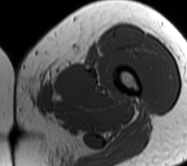
MRI of an extremity soft-tissue mass, one axial slice. Position 7 of 62 along the scan axis. MR volume resampled by the dataset authors to the PET/CT grid (not the native acquisition matrix). 3.27 mm slice thickness. 187 × 166 image matrix, field of view 183 × 162 mm. Female patient. From the clinical record (not read from this slice): histological type: leiomyosarcoma; grade: high; site of the primary tumour: groin.
Outlined on this slice (expert contour drawn on MRI and transferred to this co-registered scan by the dataset authors):
- gross tumour volume including surrounding oedema: bounding box [x1, y1, x2, y2] px = [14, 81, 44, 114]